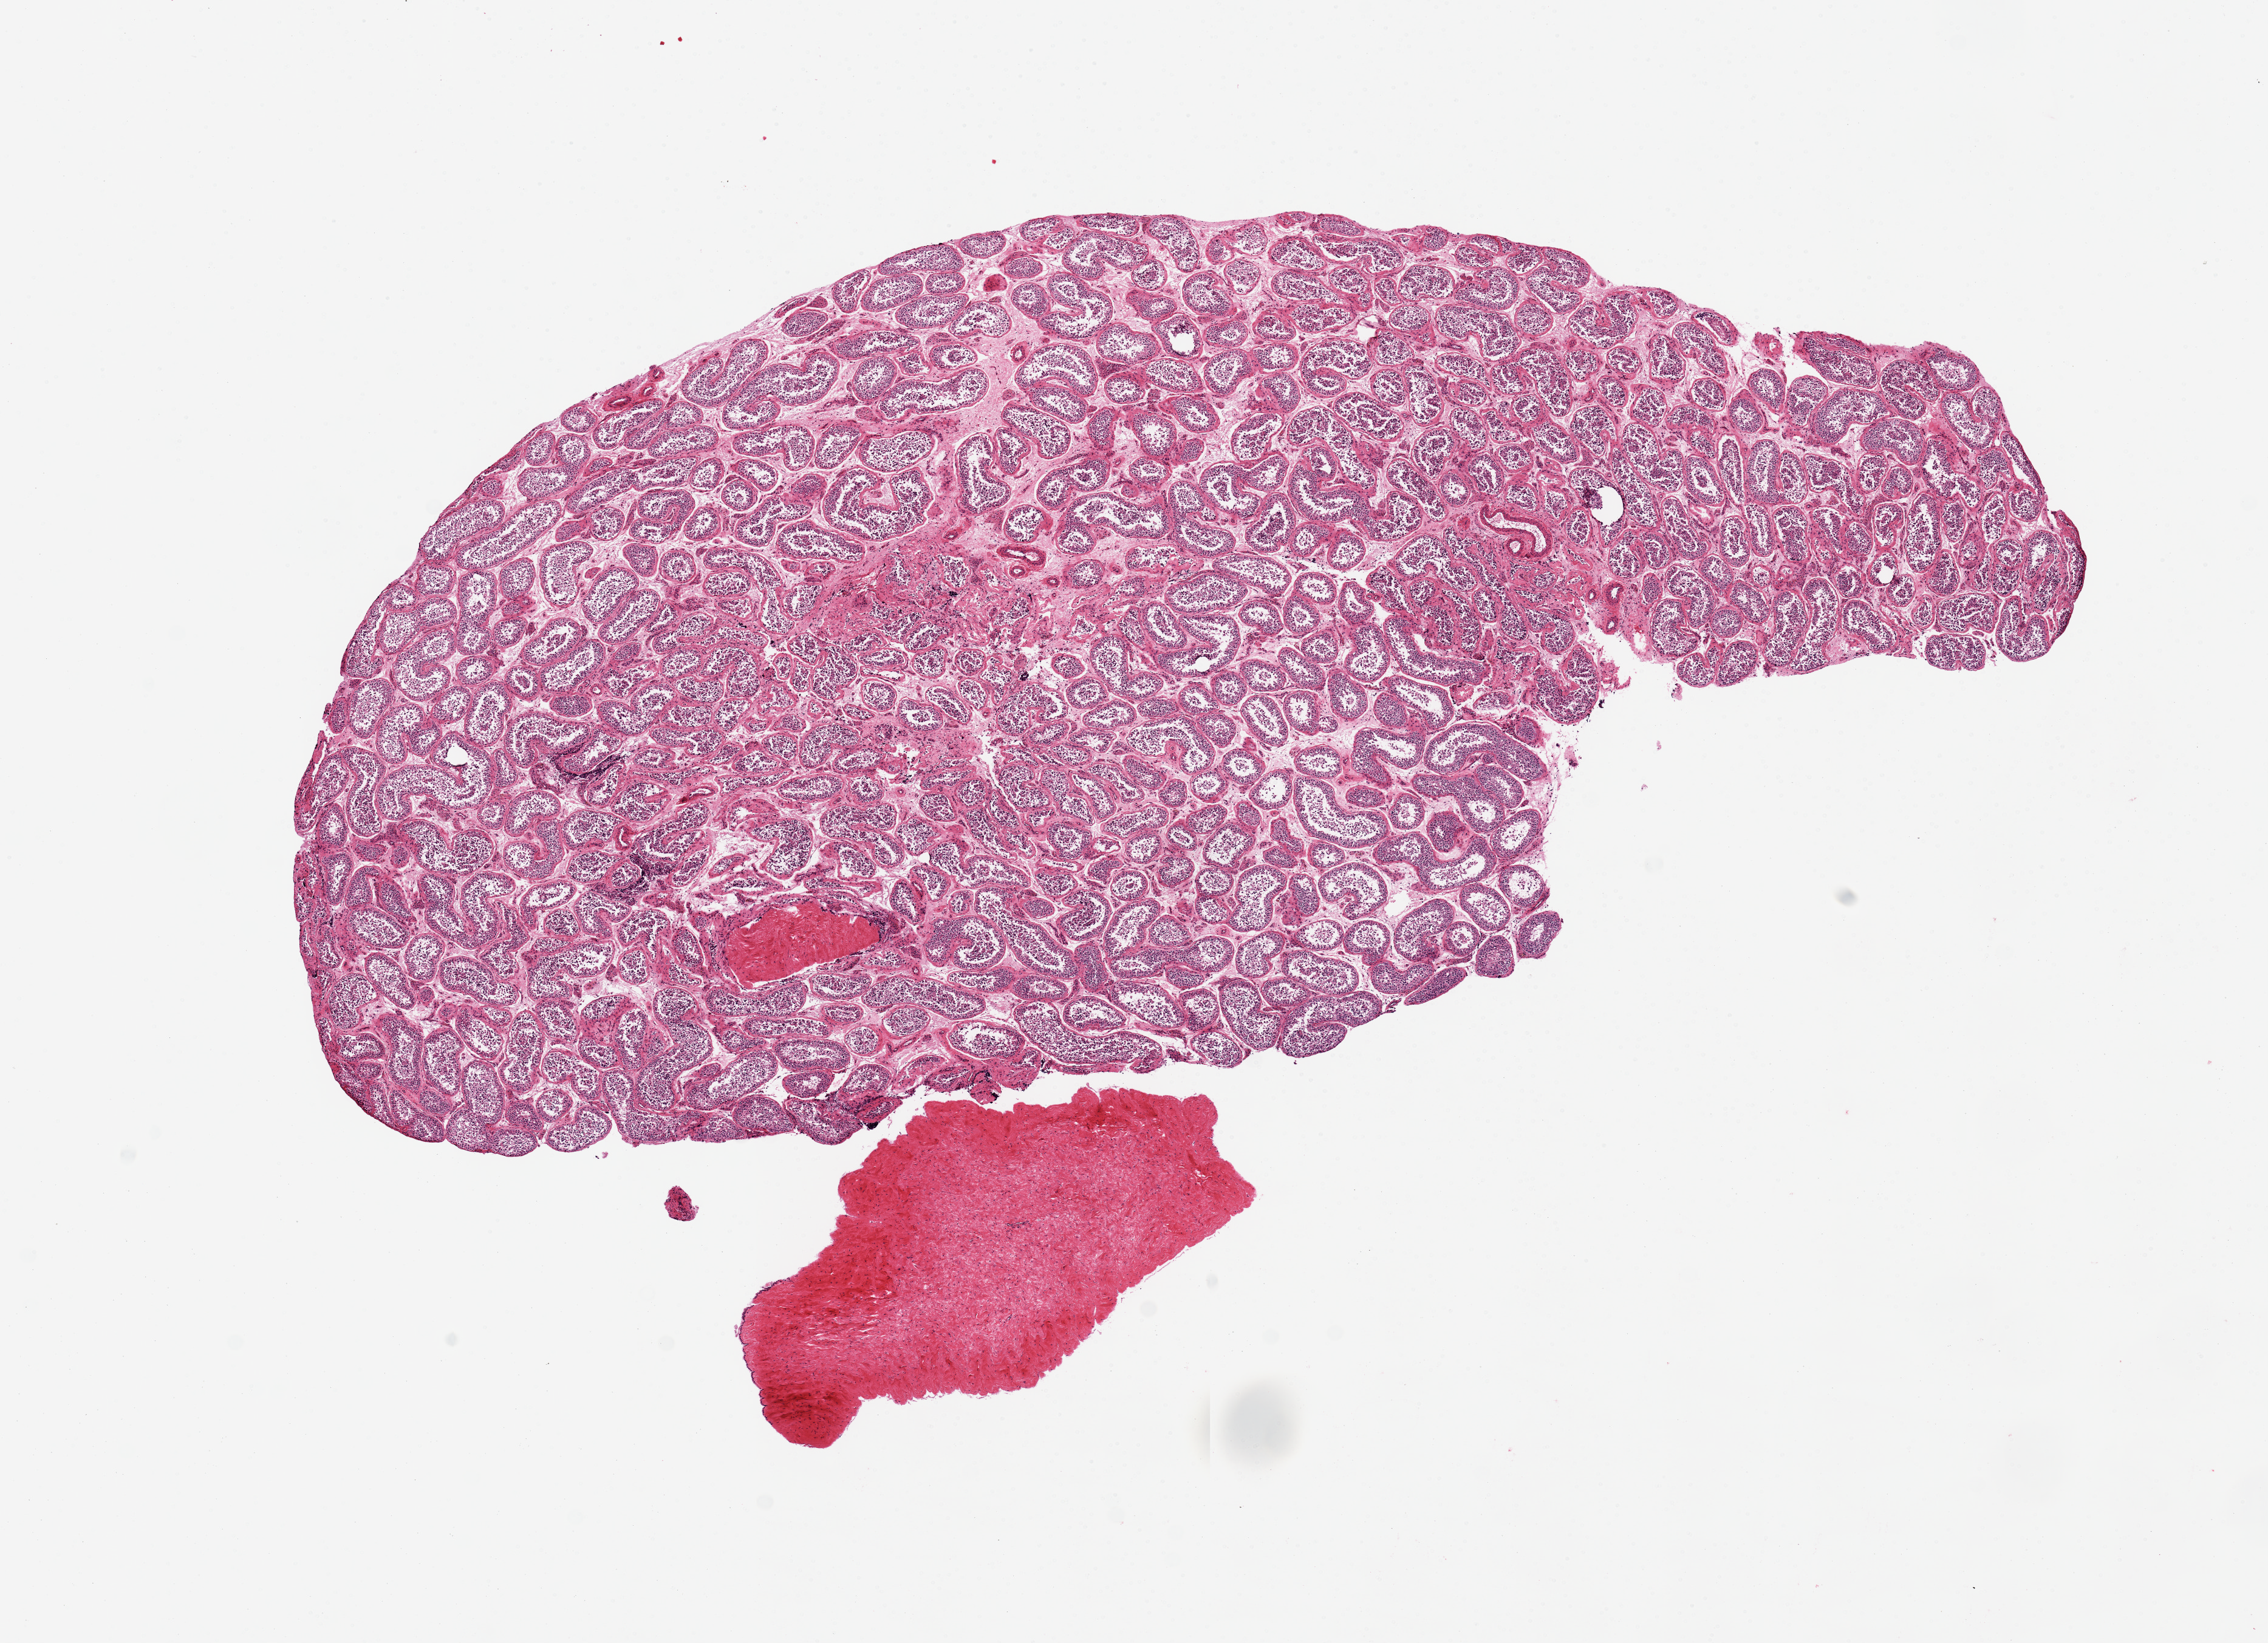
Haematoxylin and eosin whole-slide image, low-resolution overview of the scanned area, about 14.8 x 10.7 mm (slide scanned at 20x), PAXgene-fixed paraffin-embedded (PFPE) section, target tissue: testis, tissue donor sample. Donor: male.
Reviewer comment on this tissue sample: 1-2. 11.7 x 5 mm.